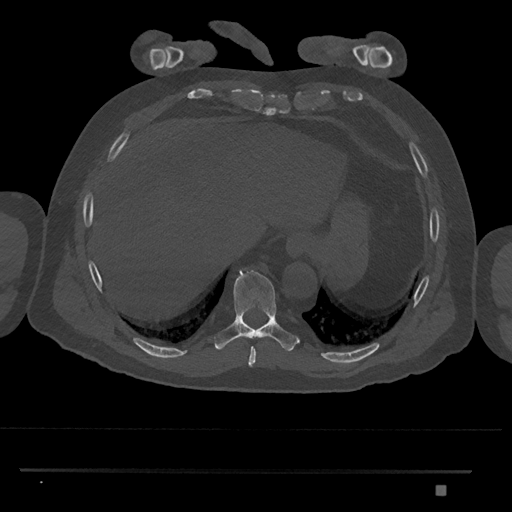
CT including the spine, one axial slice; slice 1060 of 1134 in the series (ordered by position); 120 kVp; bone window (W 1800 / L 400 HU); 512 × 512 image matrix. Male patient, age 65 years. Case-level facts recorded for this patient, not image findings: primary cancer: prostate.
Annotated regions visible in this slice (semi-automatic segmentation, software-assisted and operator-edited):
- T8 vertebra: bounding box <248,347,256,366> (left, top, right, bottom; pixels)
- T9 vertebra: <214,268,299,352>